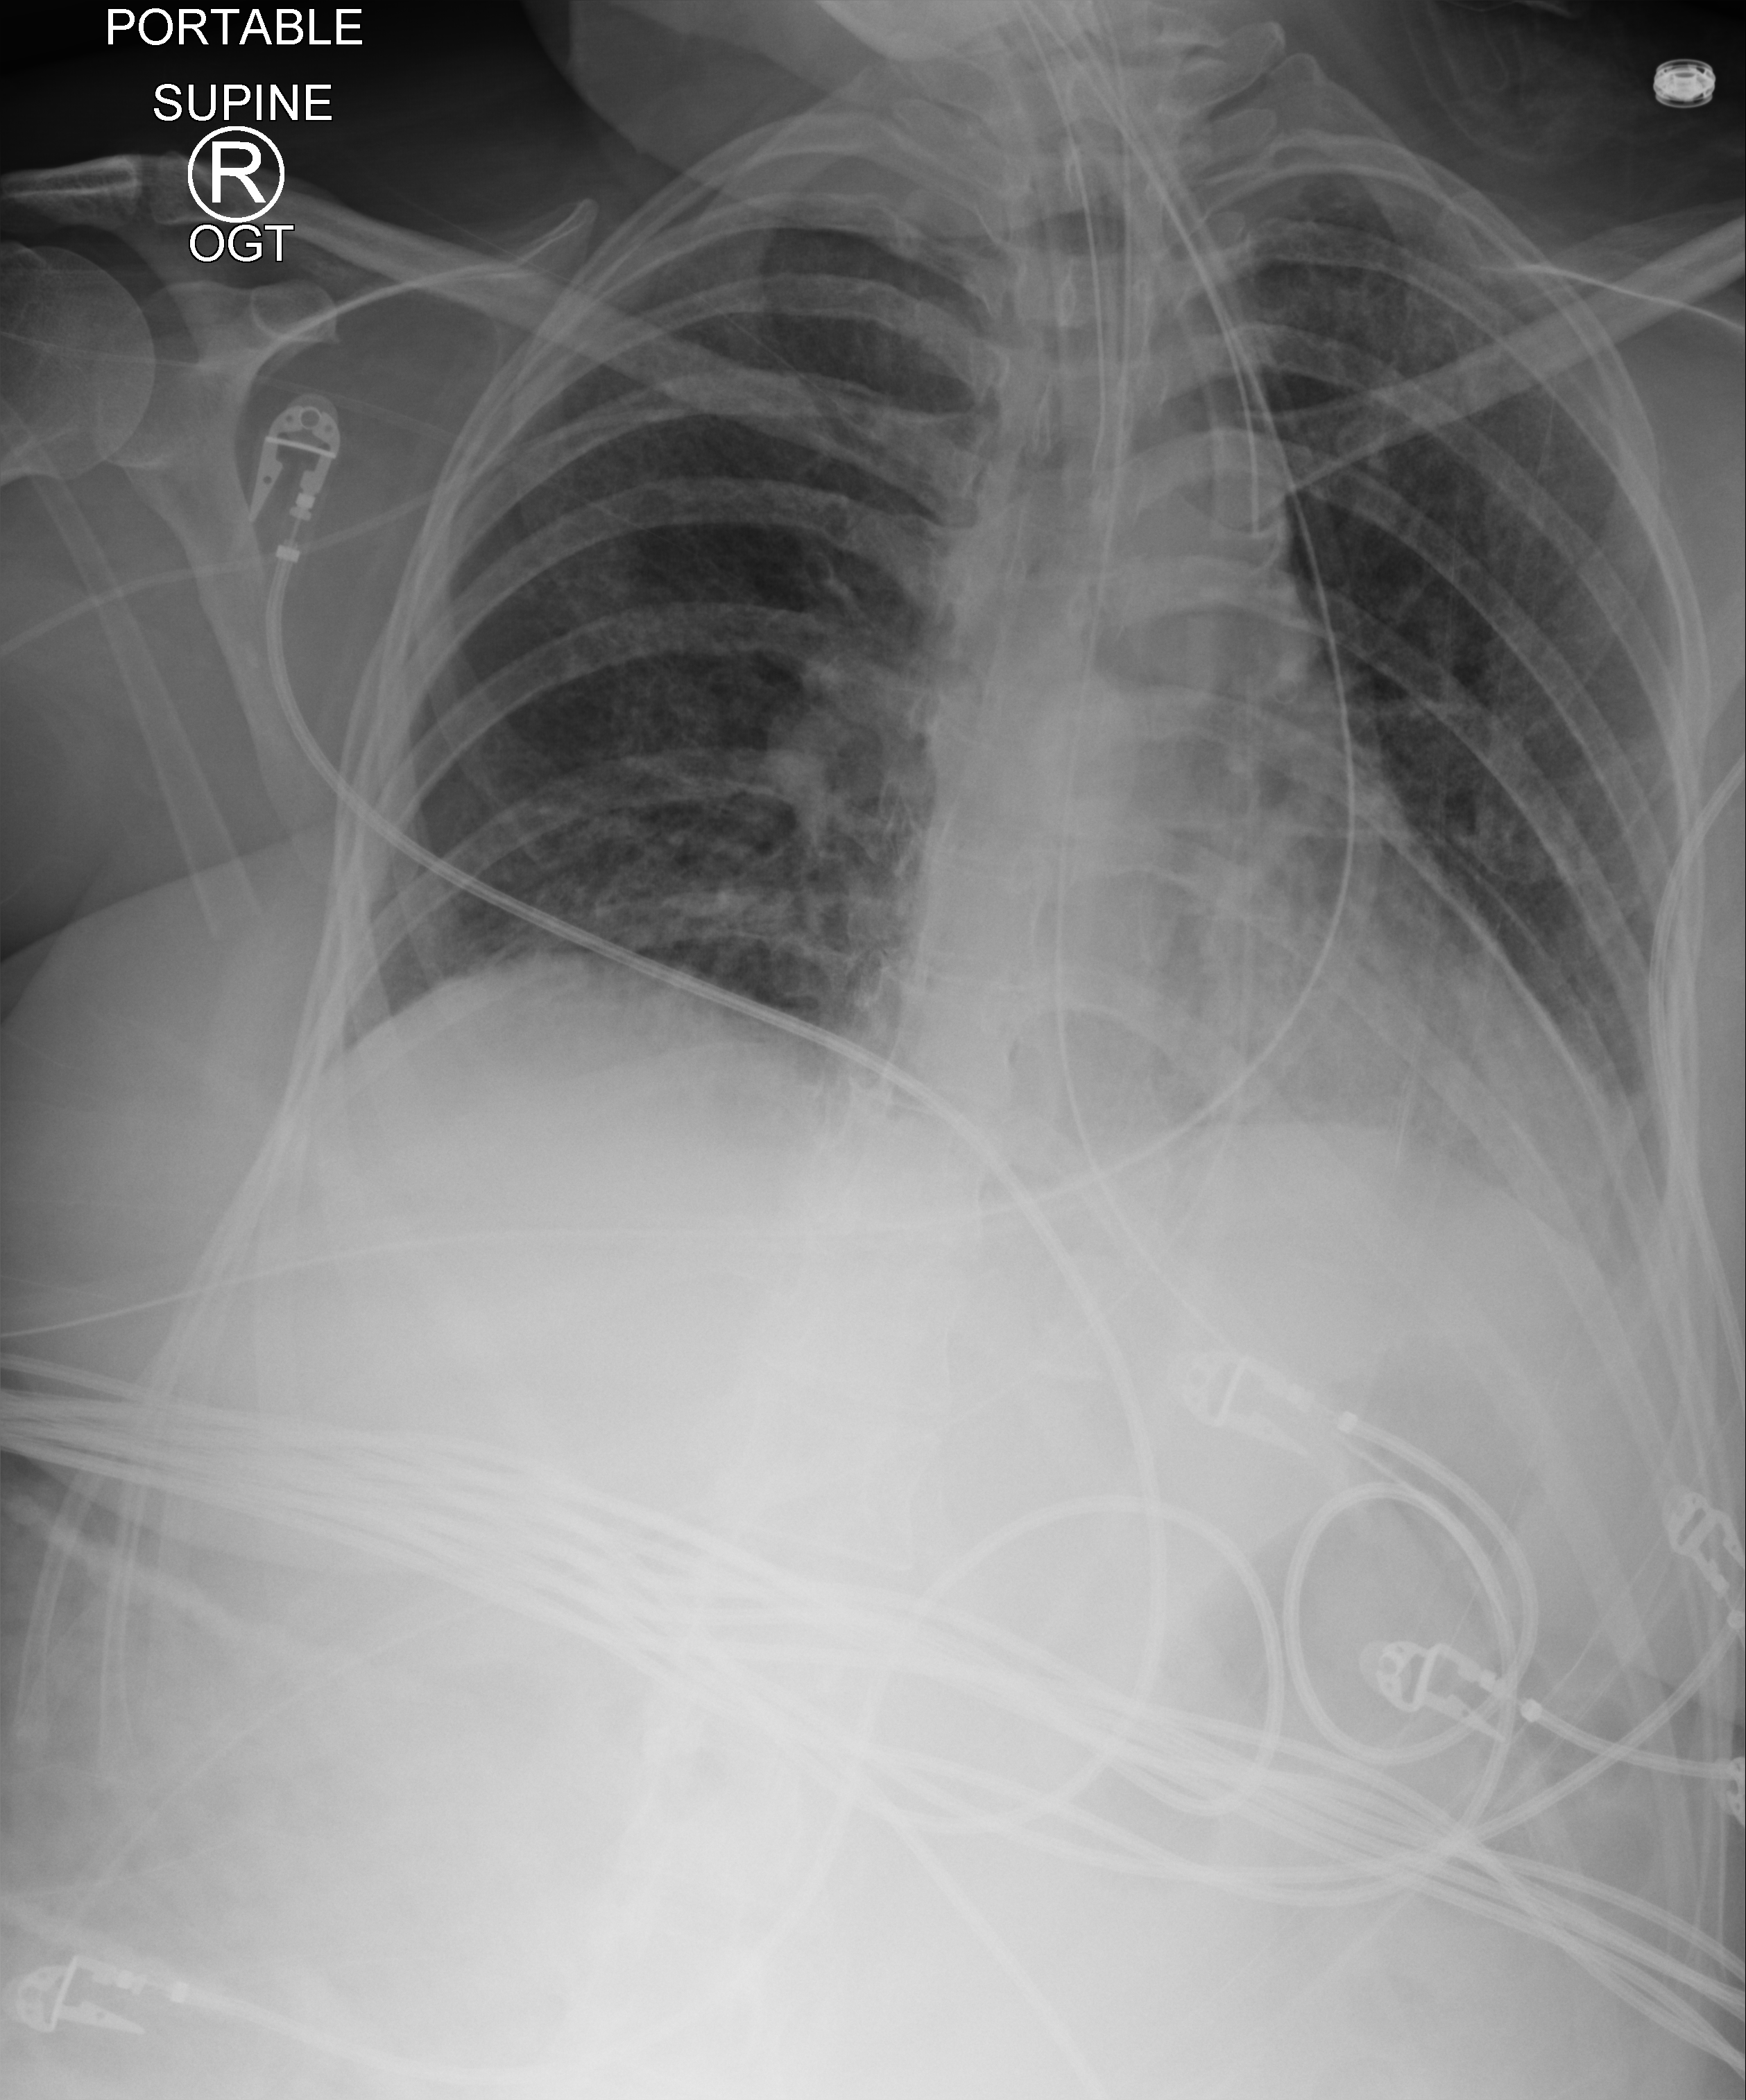
Portable chest radiograph; anteroposterior (AP) projection. Female patient hospitalised with COVID-19, age 18–59 years.
Hospital-stay facts (about this admission, not read from this image; timing relative to this image not recorded): mechanically ventilated during this hospital stay: yes; admitted to intensive care during this hospital stay: yes; length of hospital stay: 73 days.